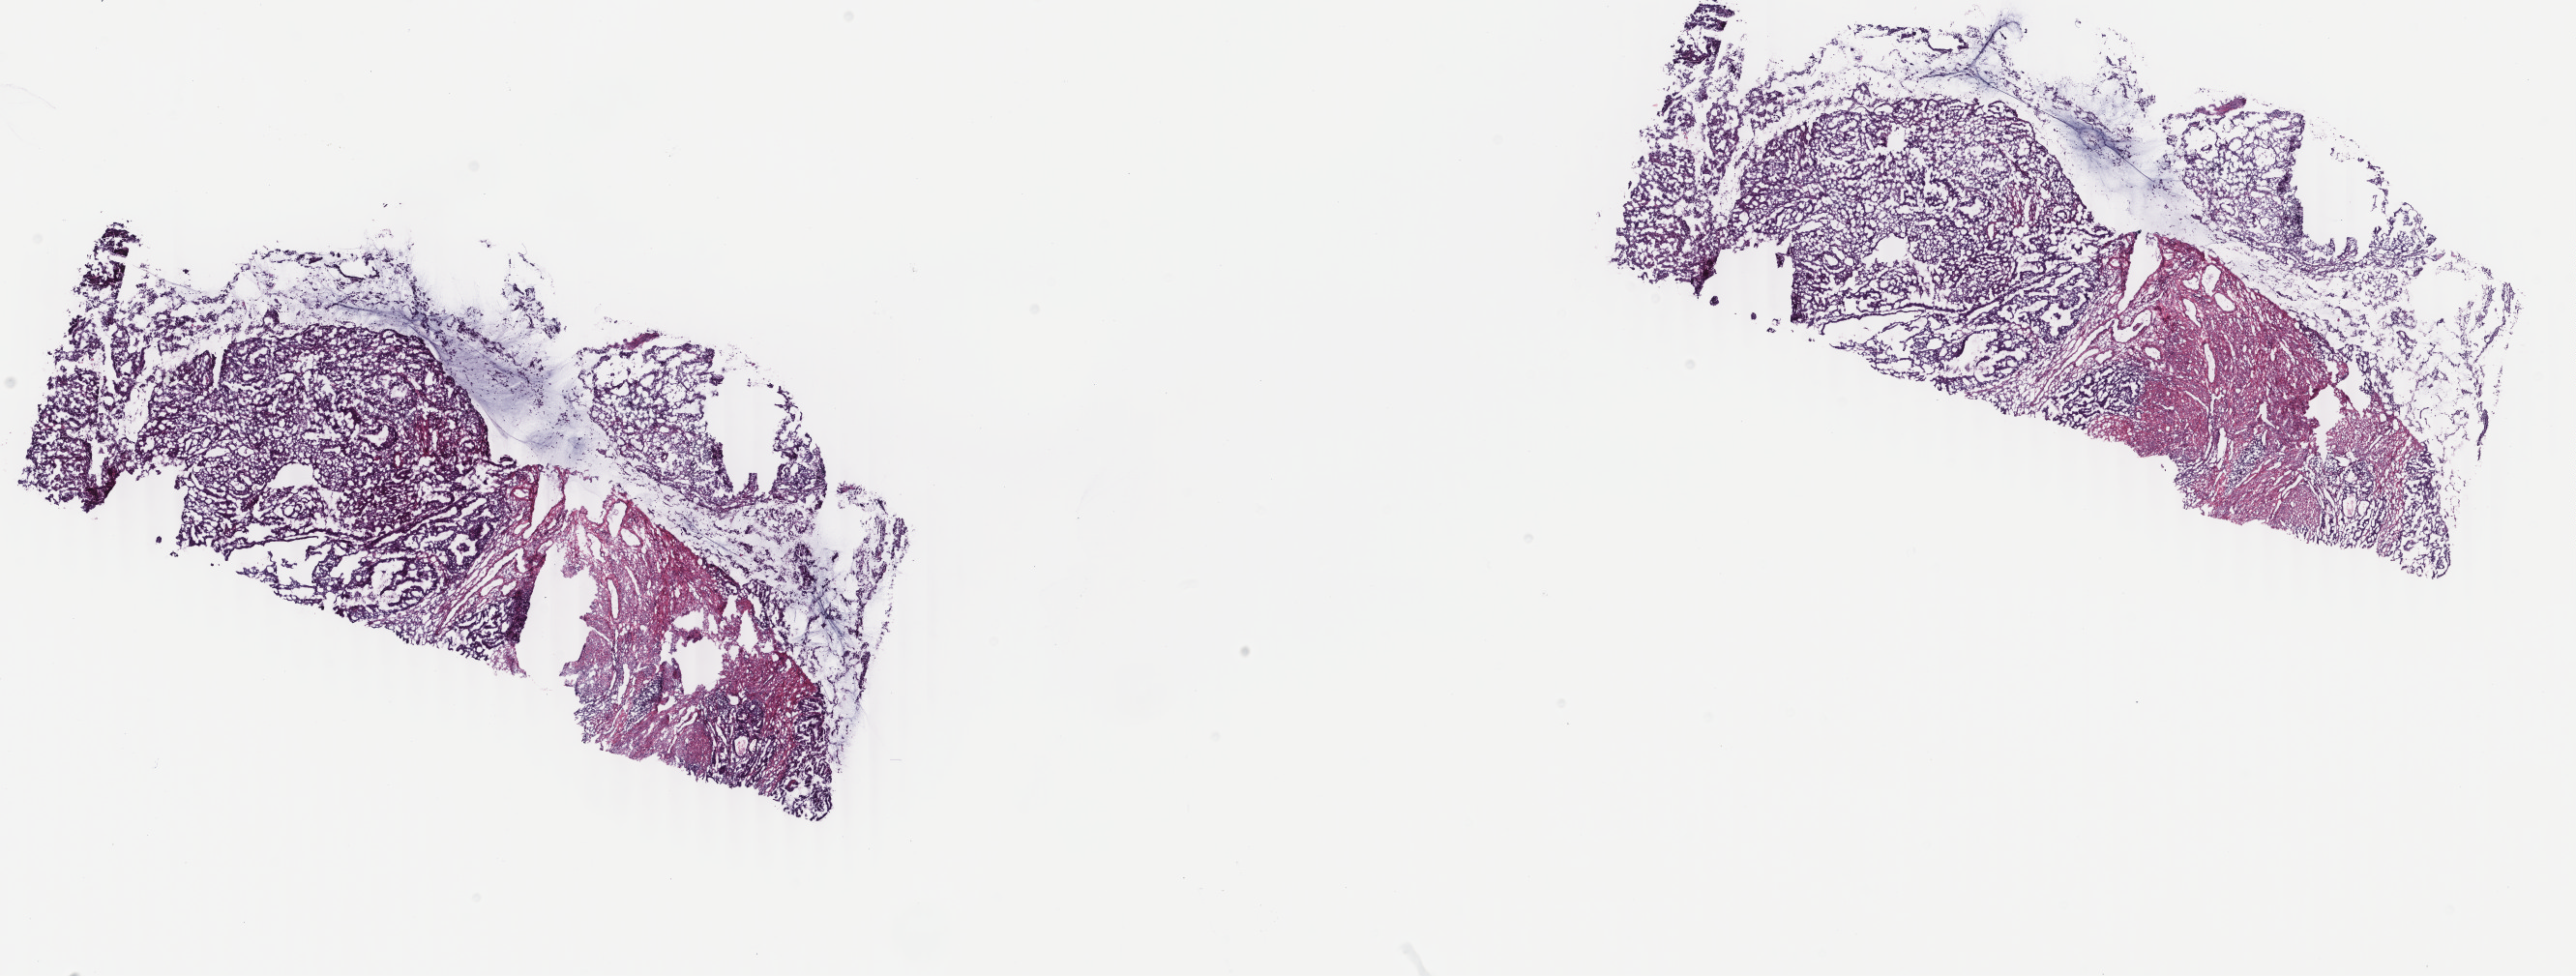
Digitized H&E tissue section (whole slide), shown as a low-resolution overview of the whole scanned area (about 21.2 x 8.0 mm), frozen section from the top of the tissue portion, primary tumour sample from the uterus. Female patient; age at initial diagnosis 60 years. Histologic grade: G2 (moderately differentiated). Slide review estimates, as recorded: tumour cells 65%, tumour nuclei 60%, normal cells 35%, stromal cells 0%, necrosis 0%. Inflammatory infiltration, as recorded: lymphocyte infiltration 0%, monocyte infiltration 0%, neutrophil infiltration 0%.
Pathologic diagnosis: Endometrioid adenocarcinoma, NOS. FIGO stage: IB.